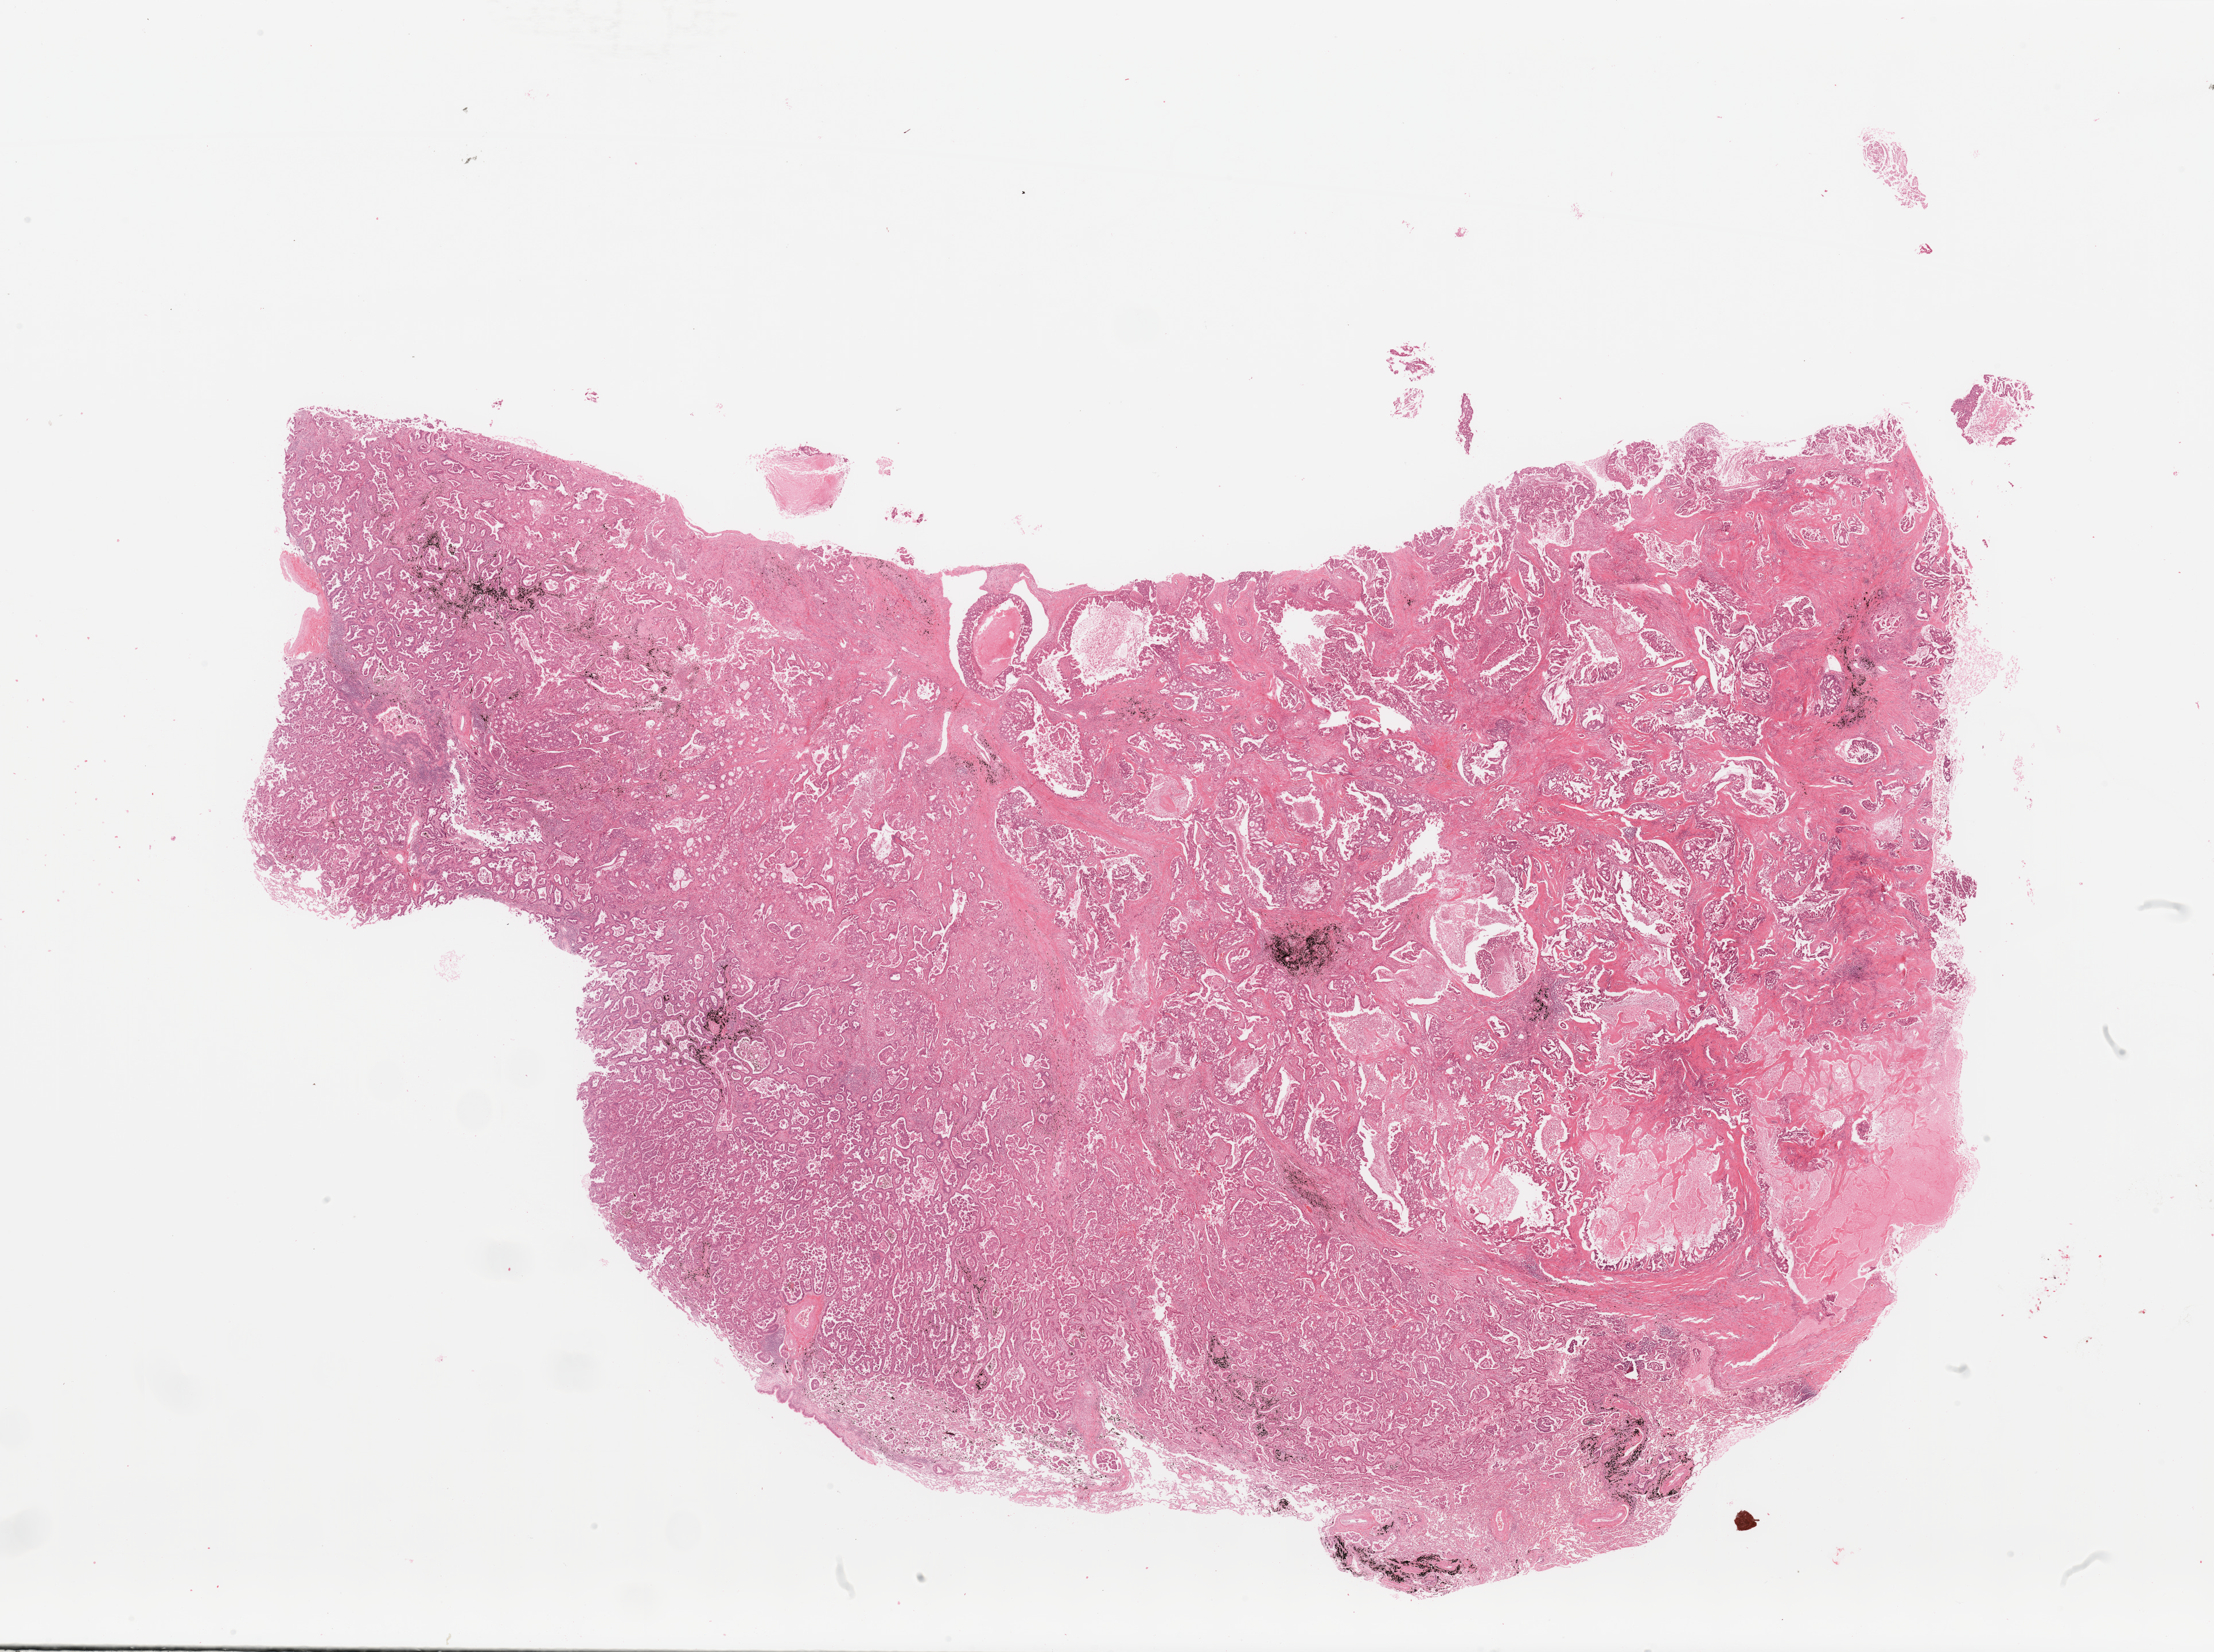
Whole-slide histology image, Hematoxylin and eosin (H&E) stained — low-resolution overview of the scanned area, about 30.5 x 22.8 mm. Tumour tissue sample, sampled site: lung. Patient: male, age 63 years.
Histologic diagnosis: Adenocarcinoma, NOS.